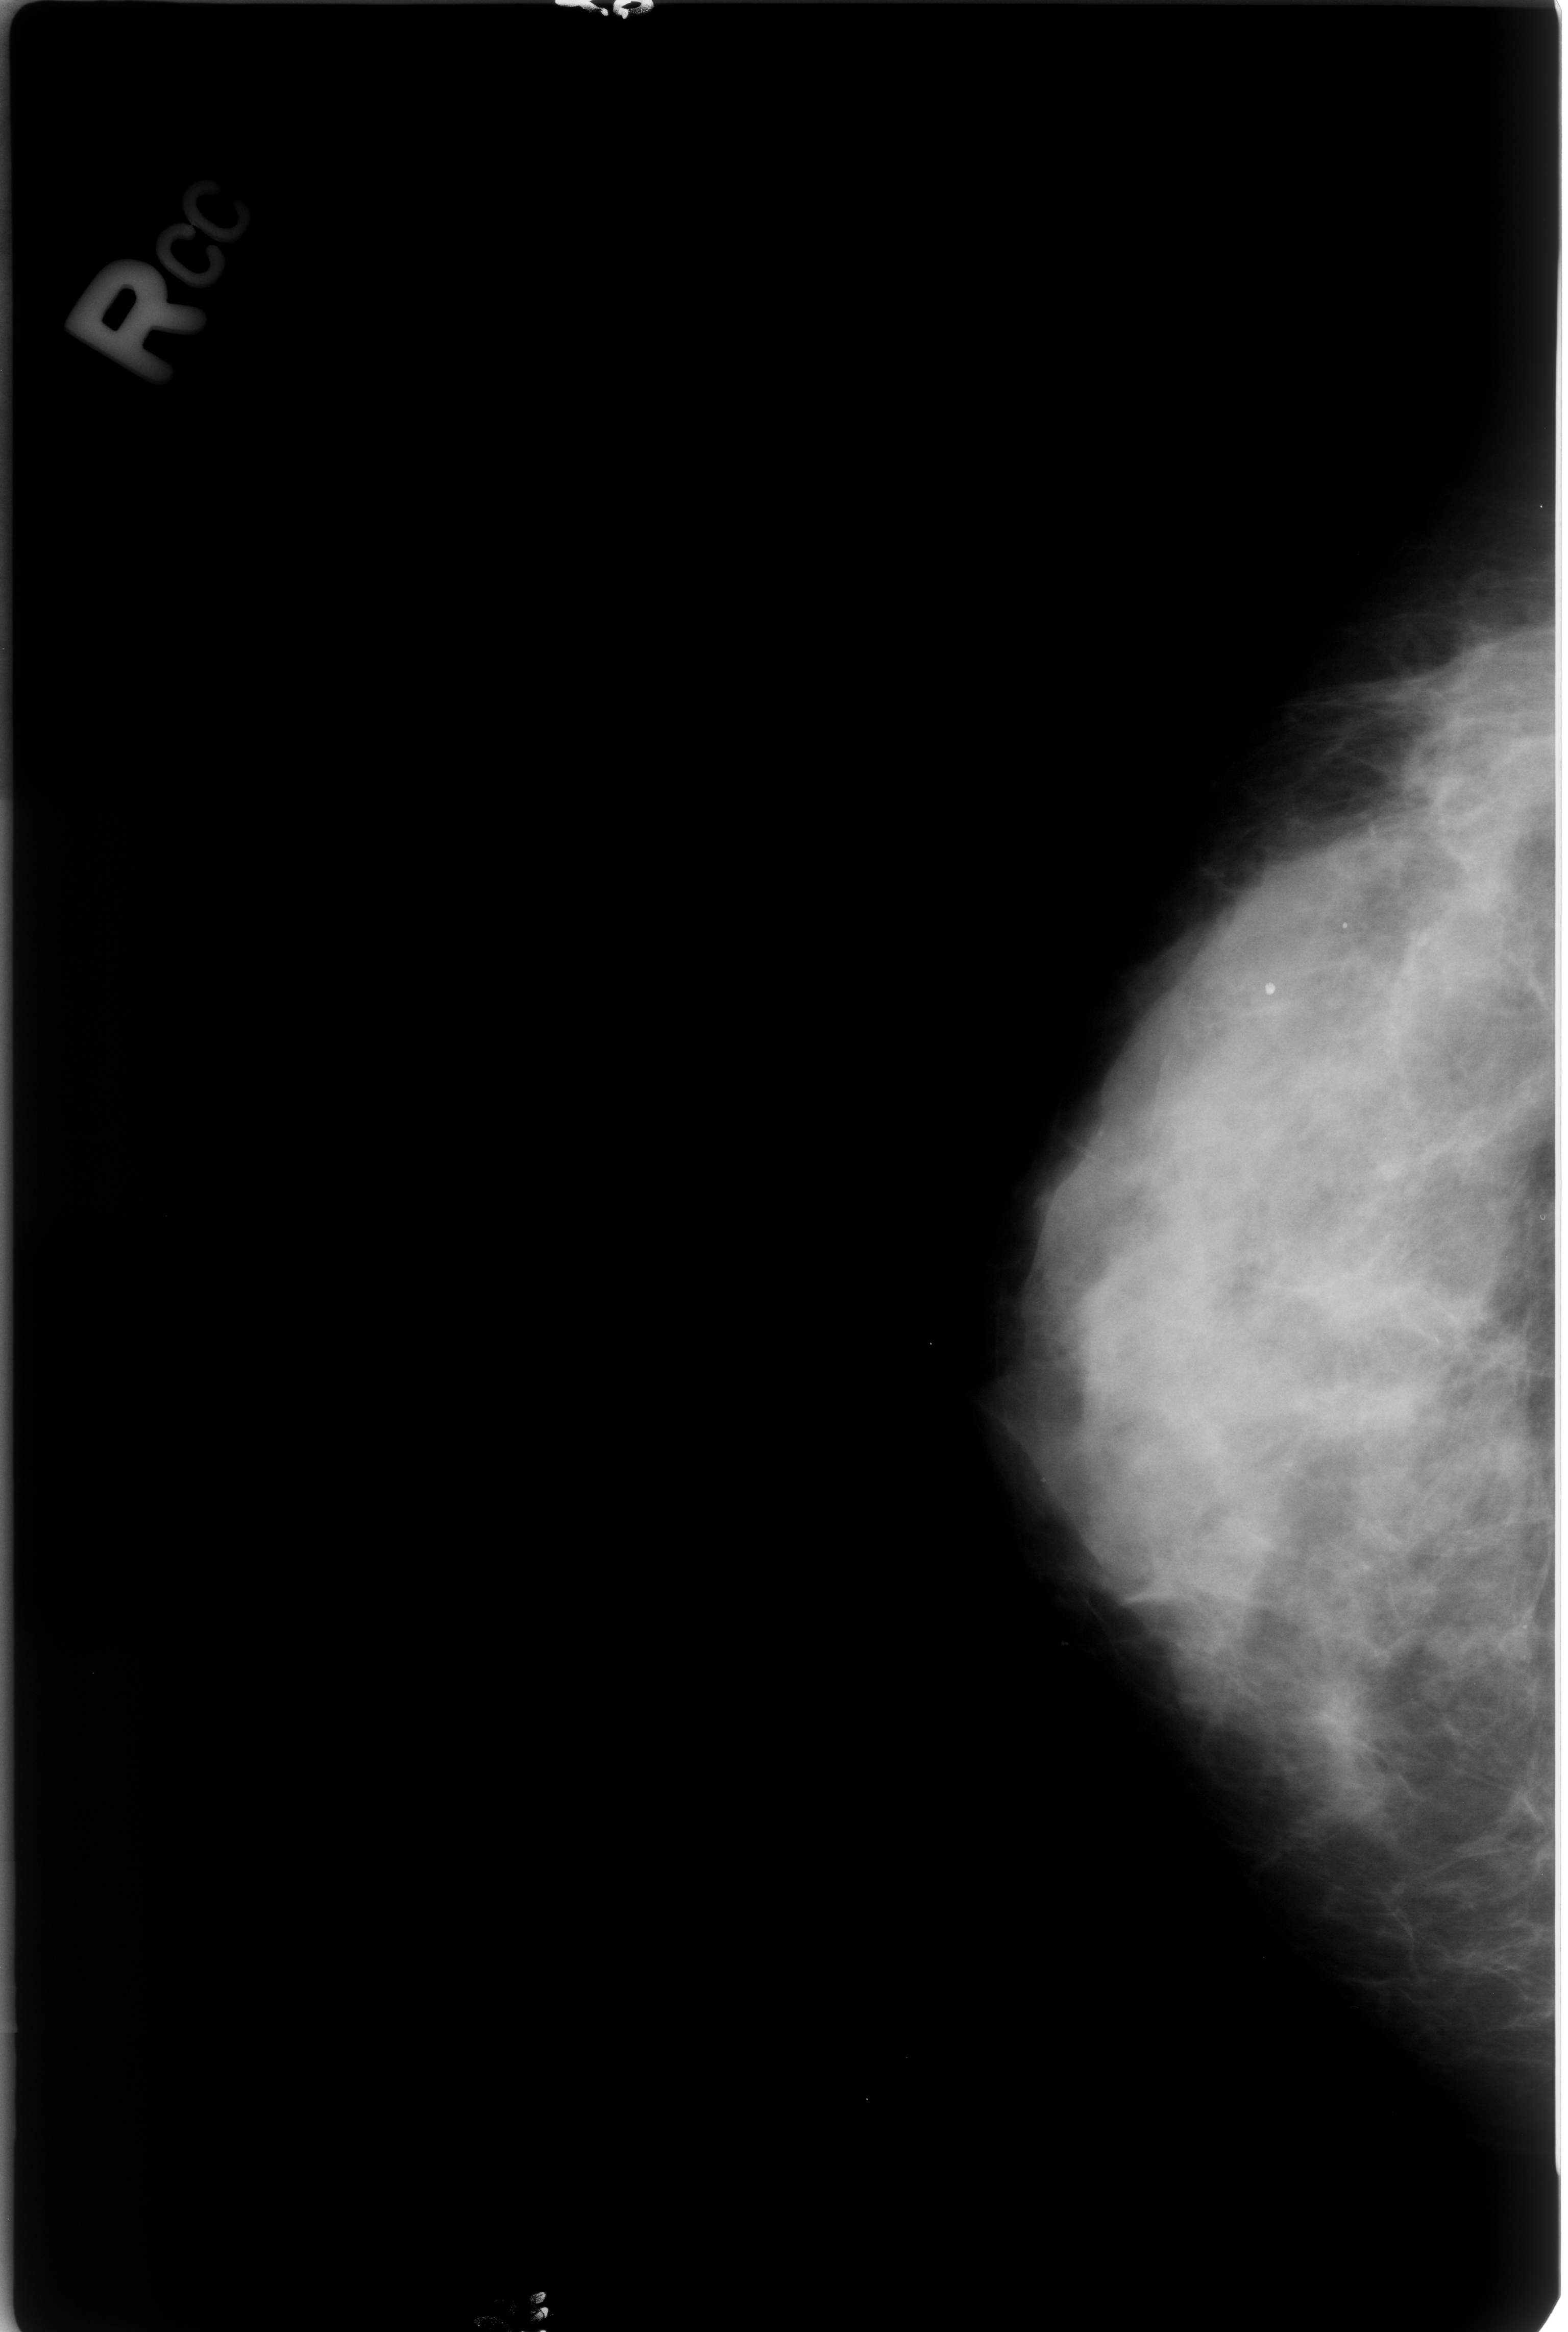
Scanned film-screen mammogram, right breast, craniocaudal (CC) view, breast composition: heterogeneously dense (BI-RADS density category 3 of 4).
Marked findings (only marked abnormalities are described; nothing is implied about the rest of the image): Finding 1 of 2: calcifications, morphology round and regular / lucent center; BI-RADS assessment category 2; benign without callback (not worked up further). Finding 2 of 2: calcifications, morphology round and regular / lucent center; BI-RADS assessment category 2; benign; no additional work-up was recommended (benign without callback).